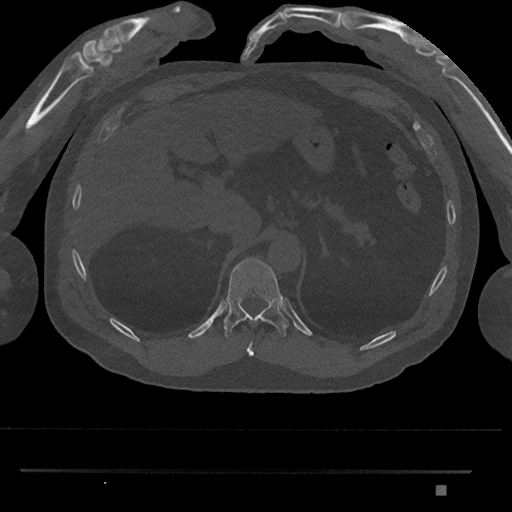
CT including the spine, one axial slice. Slice 954 of 1134 in the series (ordered by position). Reconstruction kernel Br40s/3. 120 kVp. Bone window (W 1800 / L 400 HU). 512 × 512 image matrix, field of view 429 × 429 mm. Male patient, age 65 years. From the clinical record (not read from this slice): primary cancer: prostate.
Structures marked on this image (semi-automatically segmented with operator editing):
- T10 vertebra: bounding box [x1, y1, x2, y2] px = [247, 342, 254, 356]
- T11 vertebra: [223, 257, 289, 338]